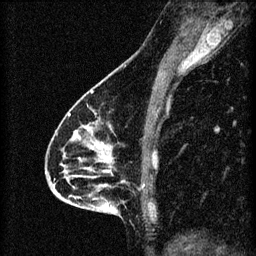
Breast MRI (dynamic contrast-enhanced), one sagittal slice. Slice 32 of 60 in the series (ordered by position). 3 images stored at this slice position (order not interpretable as contrast timing). 1.5 T. TE 4.2 ms, TR 8.2 ms. 2 mm slice thickness. 256 × 256 image matrix, field of view 180 × 180 mm. Patient: female, 46 years.
Outlined on this slice (semi-automatic segmentation, software-assisted and operator-edited):
- analysis volume of interest (the breast-tissue region the enhancement analysis was run in; not a lesion): bounding box [x1, y1, x2, y2] px = [55, 114, 148, 209]
- tumour enhancement mask (voxels above the 70 % enhancement threshold inside the analysis volume of interest): [68, 114, 113, 173]